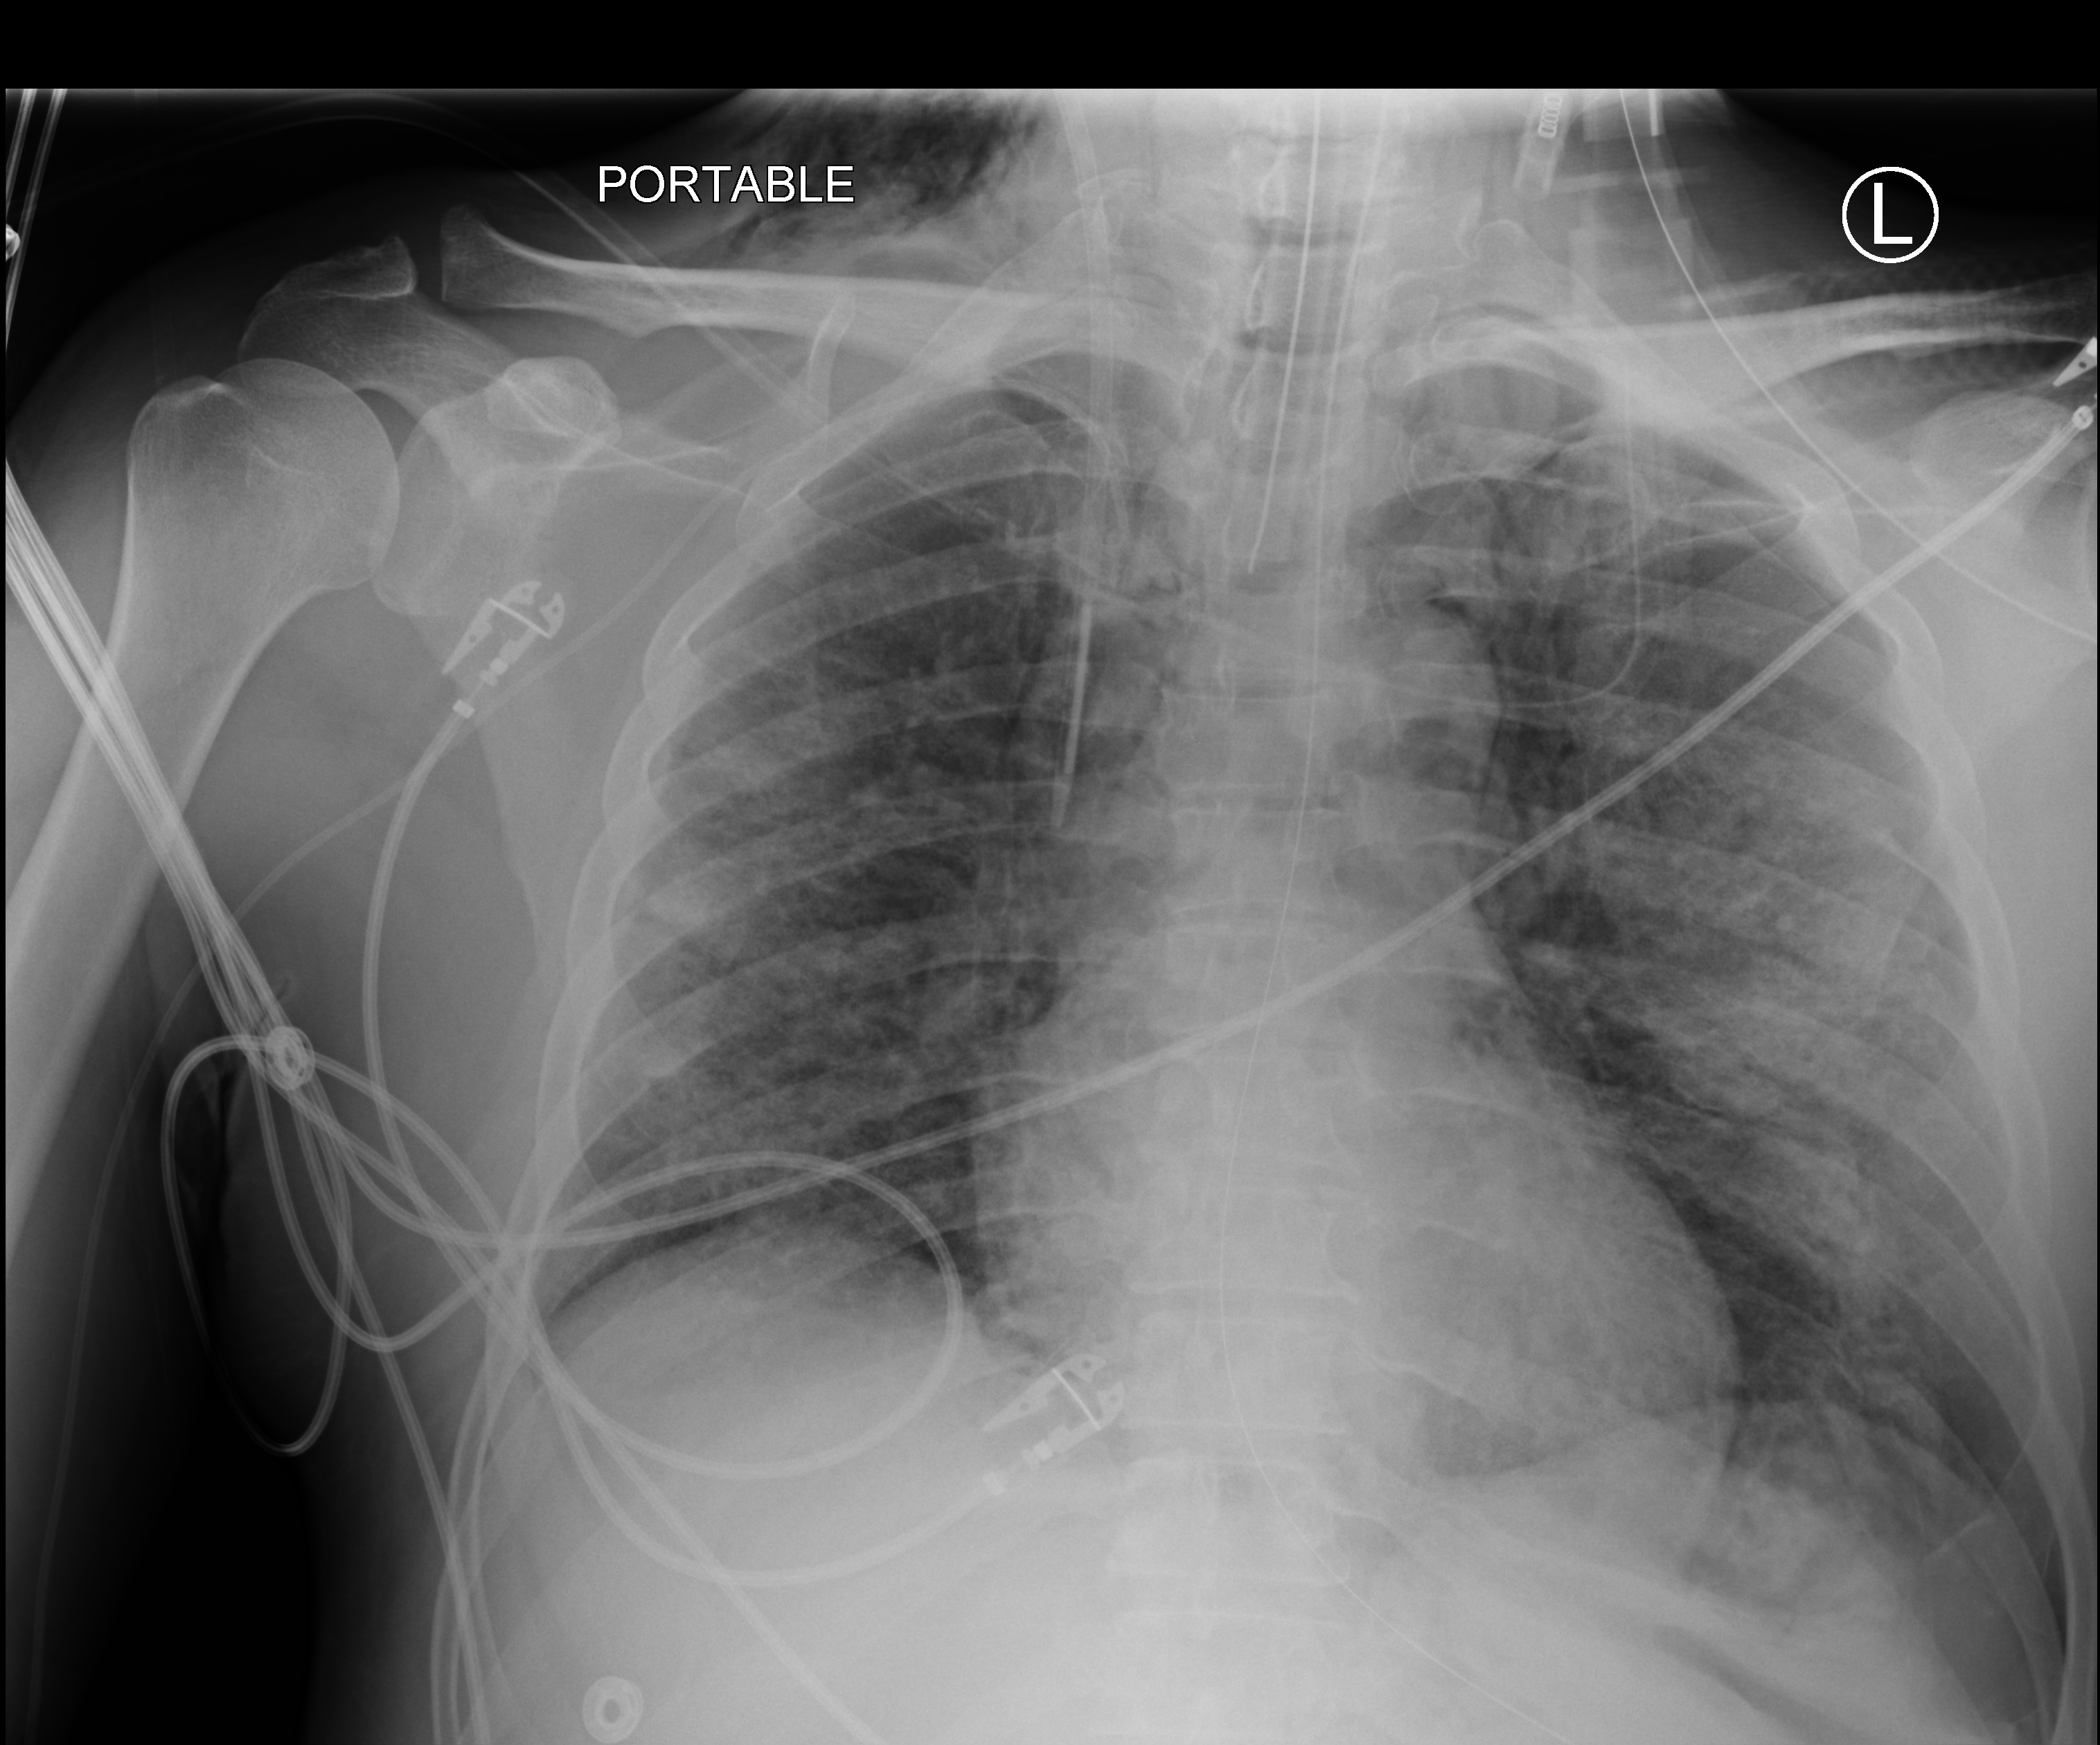
Portable chest radiograph; anteroposterior (AP) projection. Male patient hospitalised with COVID-19, age 18–59 years.
Hospital-stay facts (about this admission, not read from this image; timing relative to this image not recorded):
- COPD (admission record): no
- admitted to intensive care during this hospital stay: yes
- mechanically ventilated during this hospital stay: yes